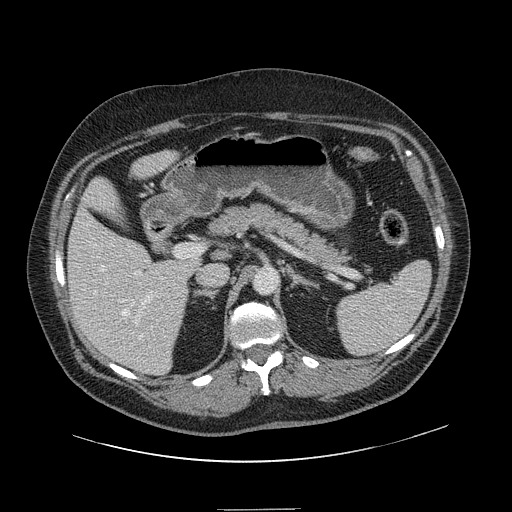
Contrast-enhanced abdominal CT, one axial slice; position 79 of 154 along the scan axis; intravenous contrast given; soft-tissue window (W 400 / L 40 HU); 2.5 mm slice thickness; 512 × 512 image matrix. Male patient, age 61 years. Case-level facts recorded for this patient, not image findings: diagnosis: colorectal cancer liver metastases, imaged before liver resection; multiple liver metastases: yes.
Annotated regions visible in this slice (expert manual segmentation):
- hepatic veins: bounding box [x1, y1, x2, y2] px = [100, 265, 153, 339]
- liver: [68, 152, 199, 374]
- planned liver remnant (the part of the liver to remain after resection): [69, 152, 200, 365]
- portal vein (with intrahepatic branches): [94, 271, 152, 323]